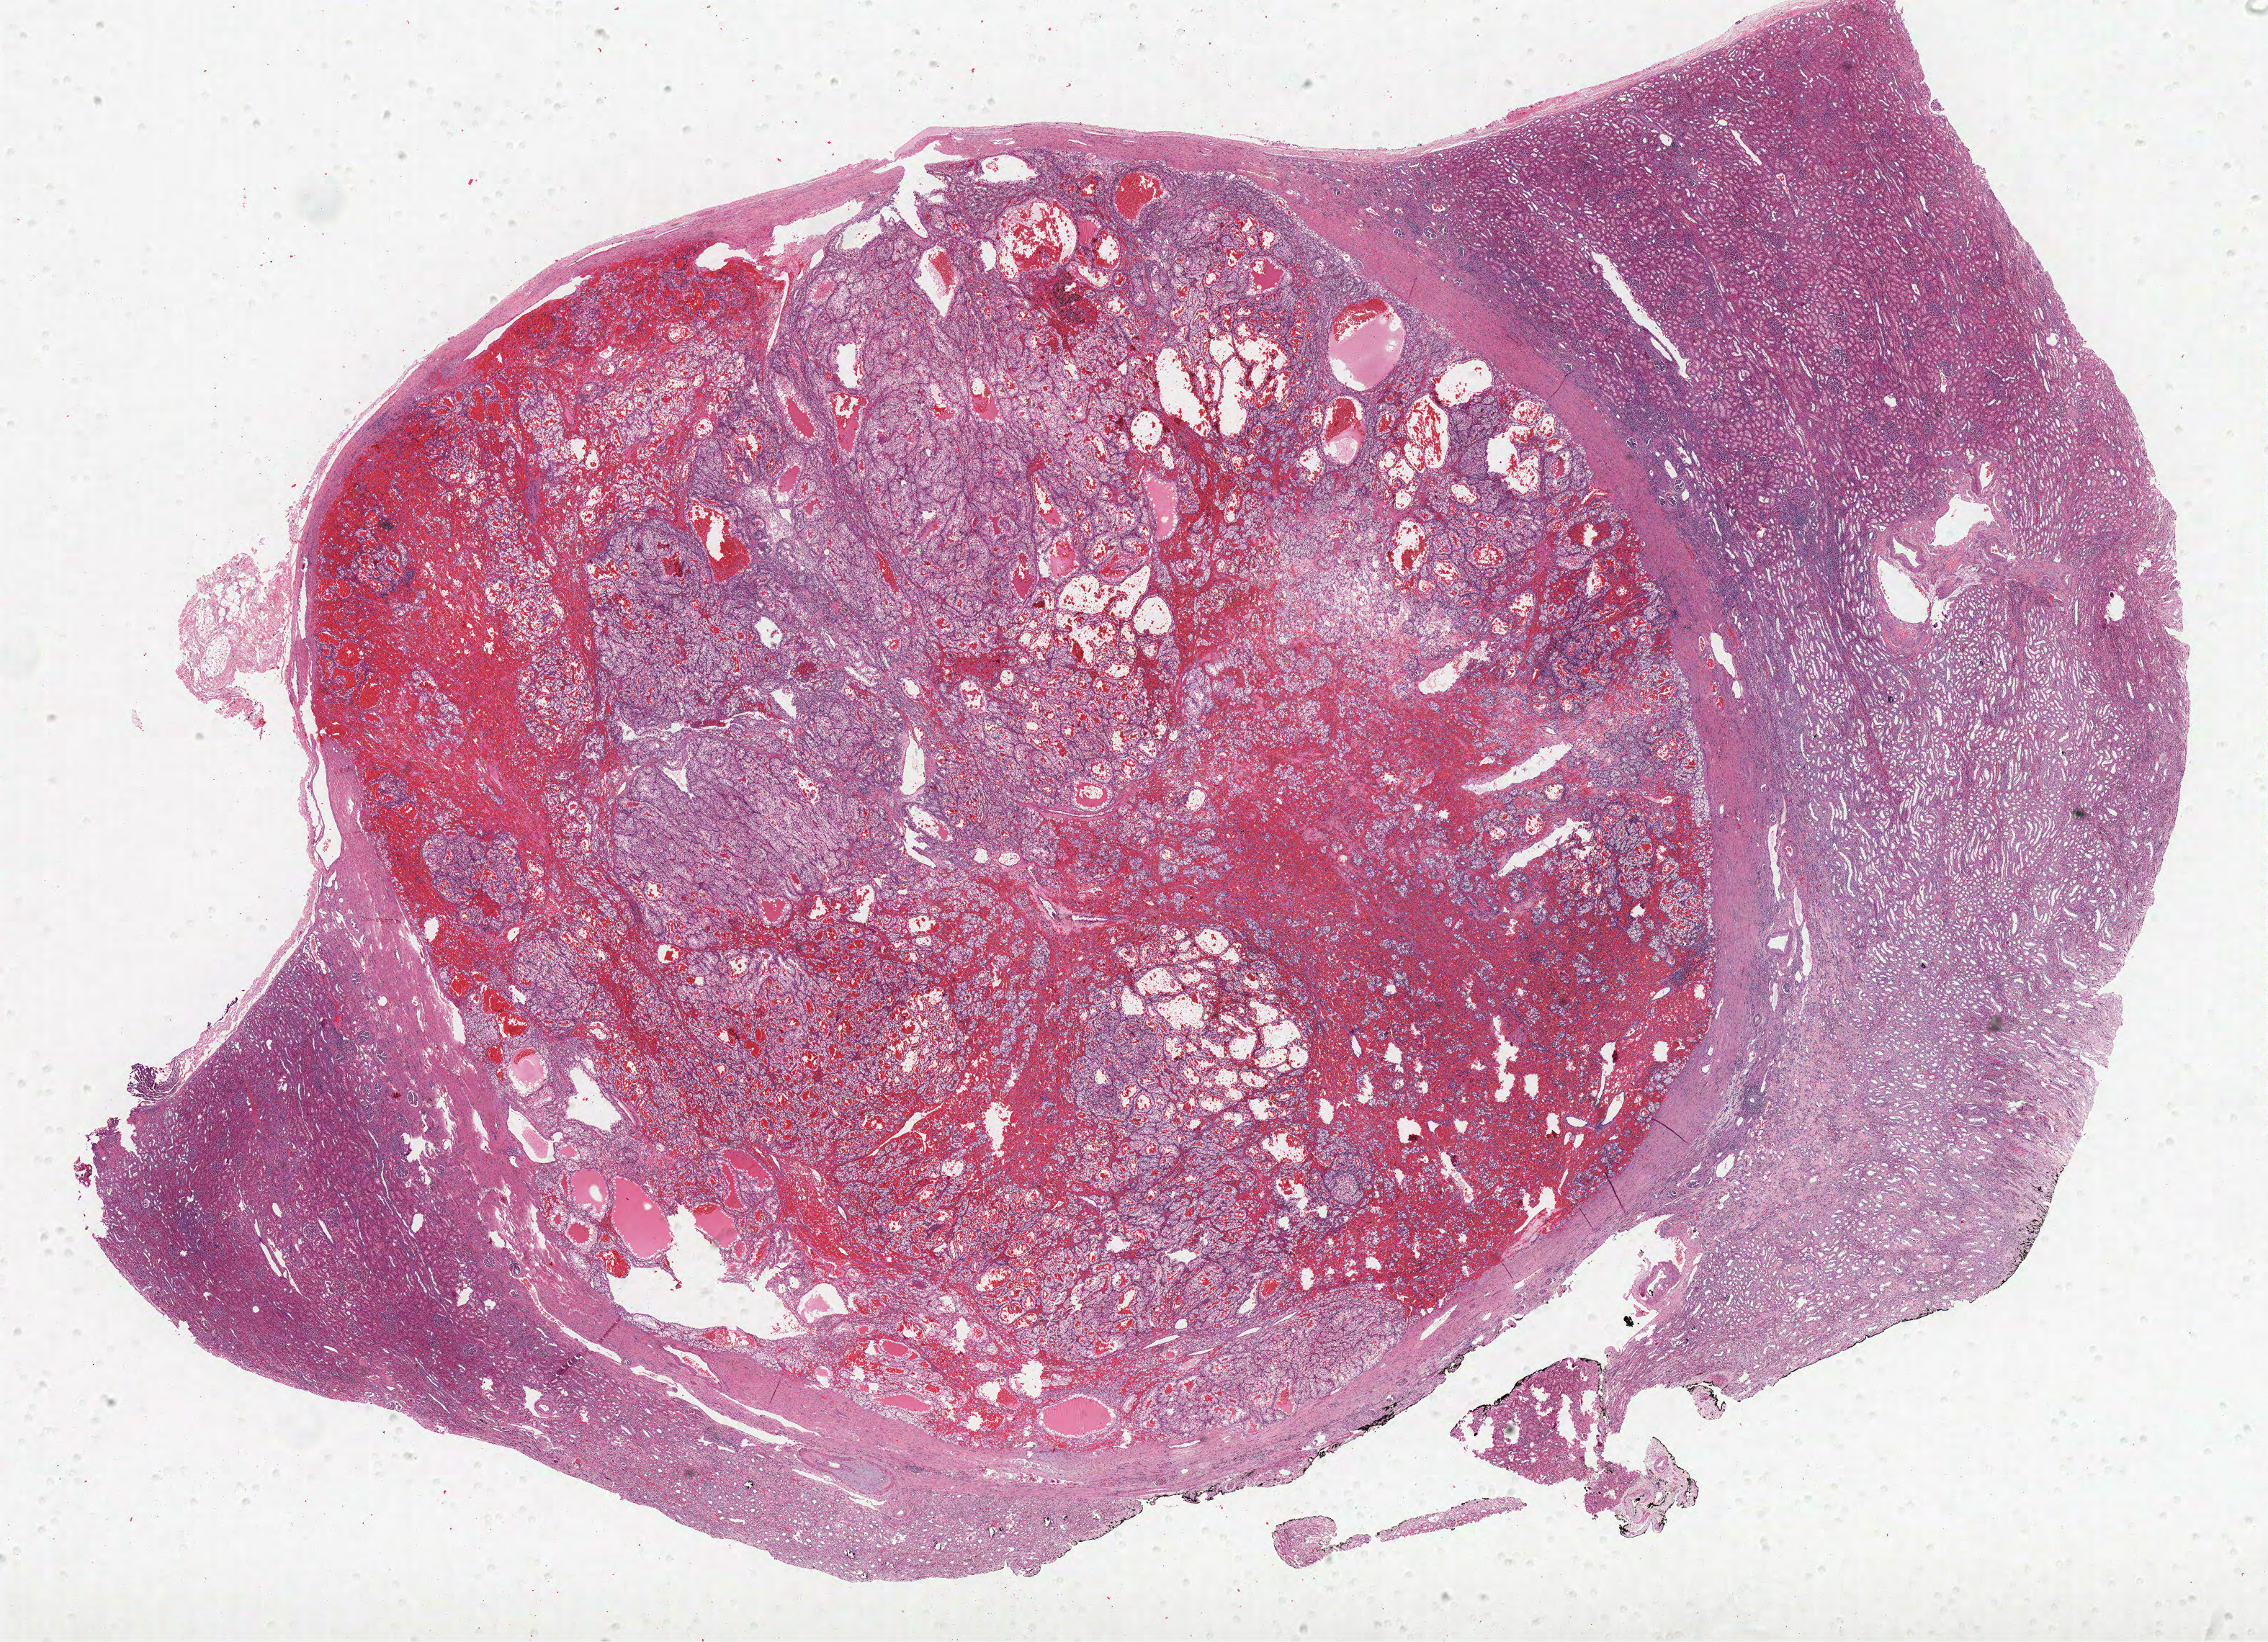
Digitized H&E-stained tissue section (whole slide) — shown as a low-resolution overview of the whole scanned area (about 25.2 x 18.2 mm), formalin-fixed paraffin-embedded (FFPE) diagnostic section, sample: primary tumour, kidney. Female, age 45 years at initial diagnosis. Histologic grade: G2 (moderately differentiated).
Laterality: left. Pathologic diagnosis: Clear cell adenocarcinoma, NOS. TNM: T1a NX M0. AJCC pathologic stage: I.